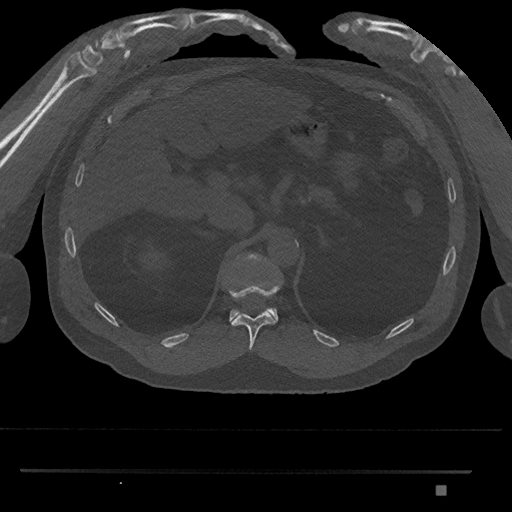
CT including the spine, one axial slice; slice 928 of 1134 in the series (ordered by position); reconstruction kernel Br40s/3; 120 kVp; bone window (W 1800 / L 400 HU); 0.5 mm slice thickness; 512 × 512 image matrix, field of view 429 × 429 mm. Male patient, age 65 years. From the clinical record (not read from this slice): primary cancer: prostate.
Annotated regions visible in this slice (semi-automatic segmentation, software-assisted and operator-edited):
- T11 vertebra: box from (x=228, y=286) to (x=280, y=350) px
- T12 vertebra: (x=229, y=253)–(x=278, y=322)